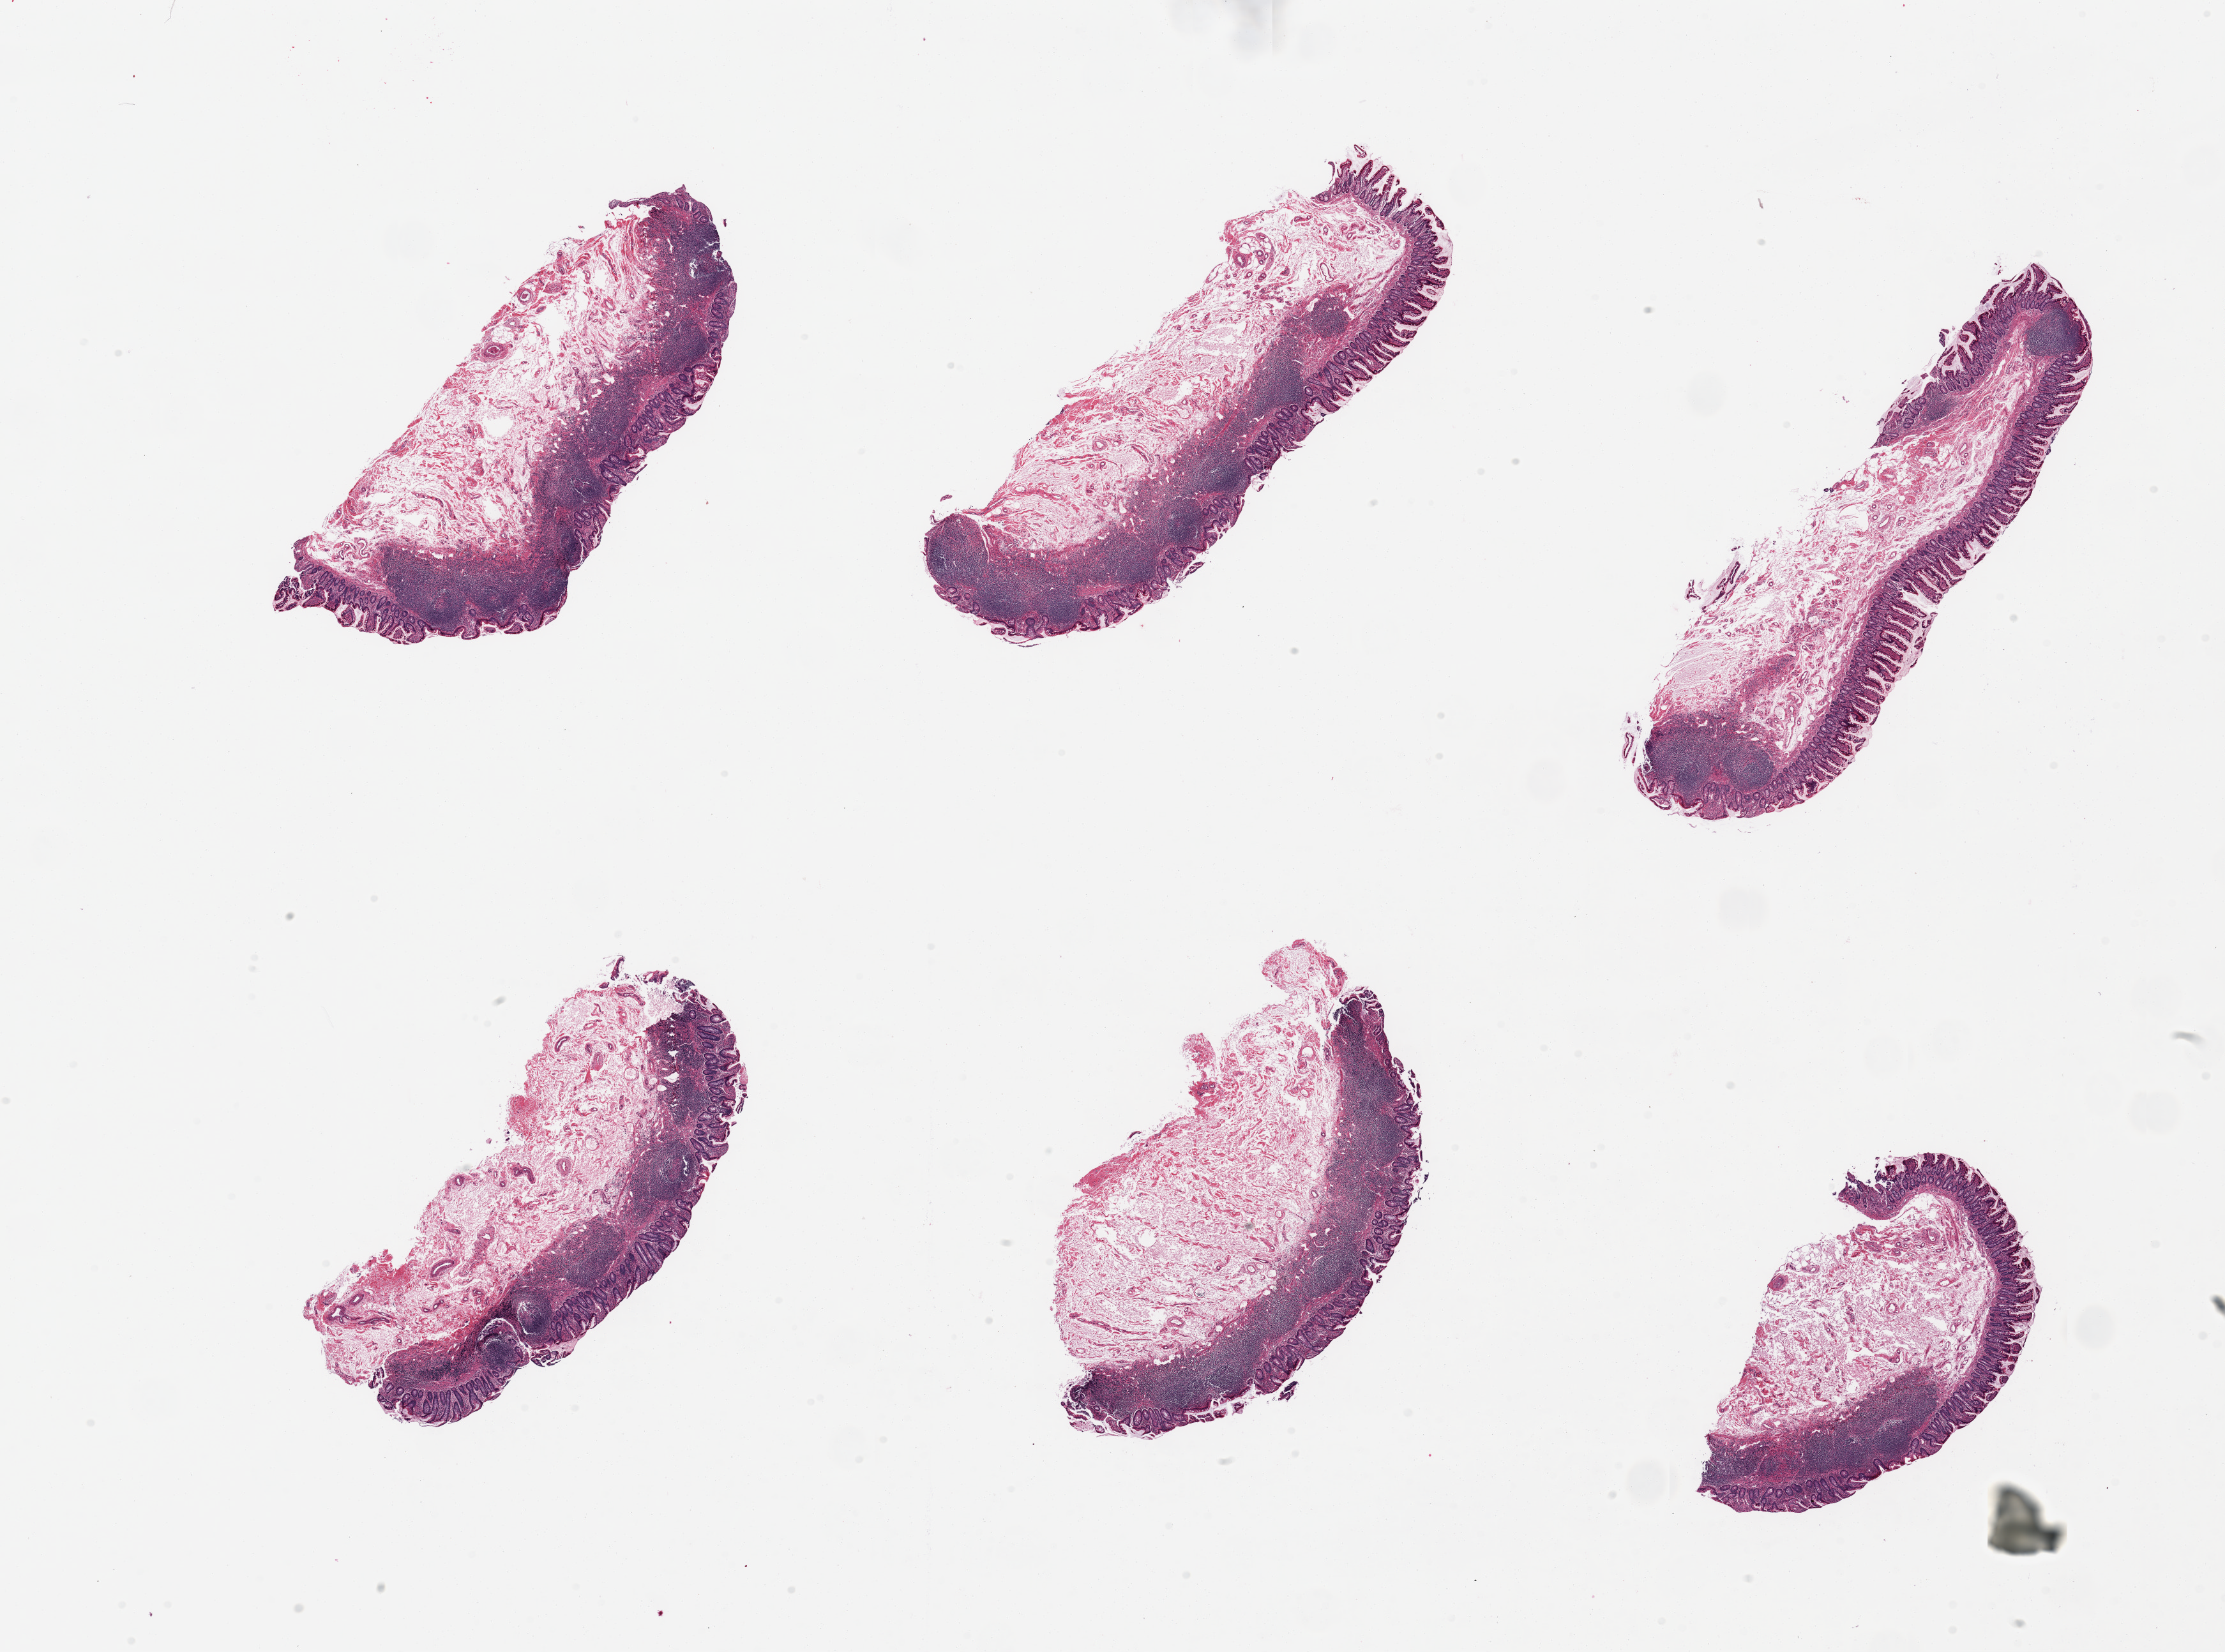
Whole-slide image, haematoxylin and eosin stain, brightfield — a low-resolution overview of the entire scanned area, about 27.6 x 20.5 mm (acquisition: 20x scan); PAXgene-fixed paraffin-embedded (PFPE) section; target tissue: ileum; donor tissue sample. Donor sex: male.
- reviewer comment on this tissue sample: 6 pieces, abundant target lymphoid aggregates are ~30% of tissue